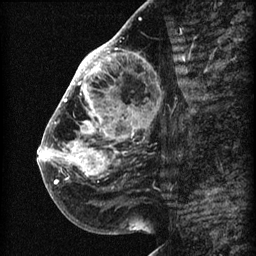
Breast MRI (dynamic contrast-enhanced), one sagittal slice. Slice 29 of 60 in the series (ordered by position). 3 images stored at this slice position (order not interpretable as contrast timing). 1.5 T. TE 4.2 ms, TR 22.7 ms. 2 mm slice thickness. 256 × 256 image matrix. Female patient, age 48 years. From the clinical record (not read from this slice): setting: breast cancer imaged before/during neoadjuvant chemotherapy; receptor status: triple-negative.
Annotated regions visible in this slice (semi-automatically segmented with operator editing):
- analysis volume of interest (the breast-tissue region the enhancement analysis was run in; not a lesion): bounding box <44,30,173,207> (left, top, right, bottom; pixels)
- tumour enhancement mask (voxels above the 90 % enhancement threshold inside the analysis volume of interest): <44,30,129,189>